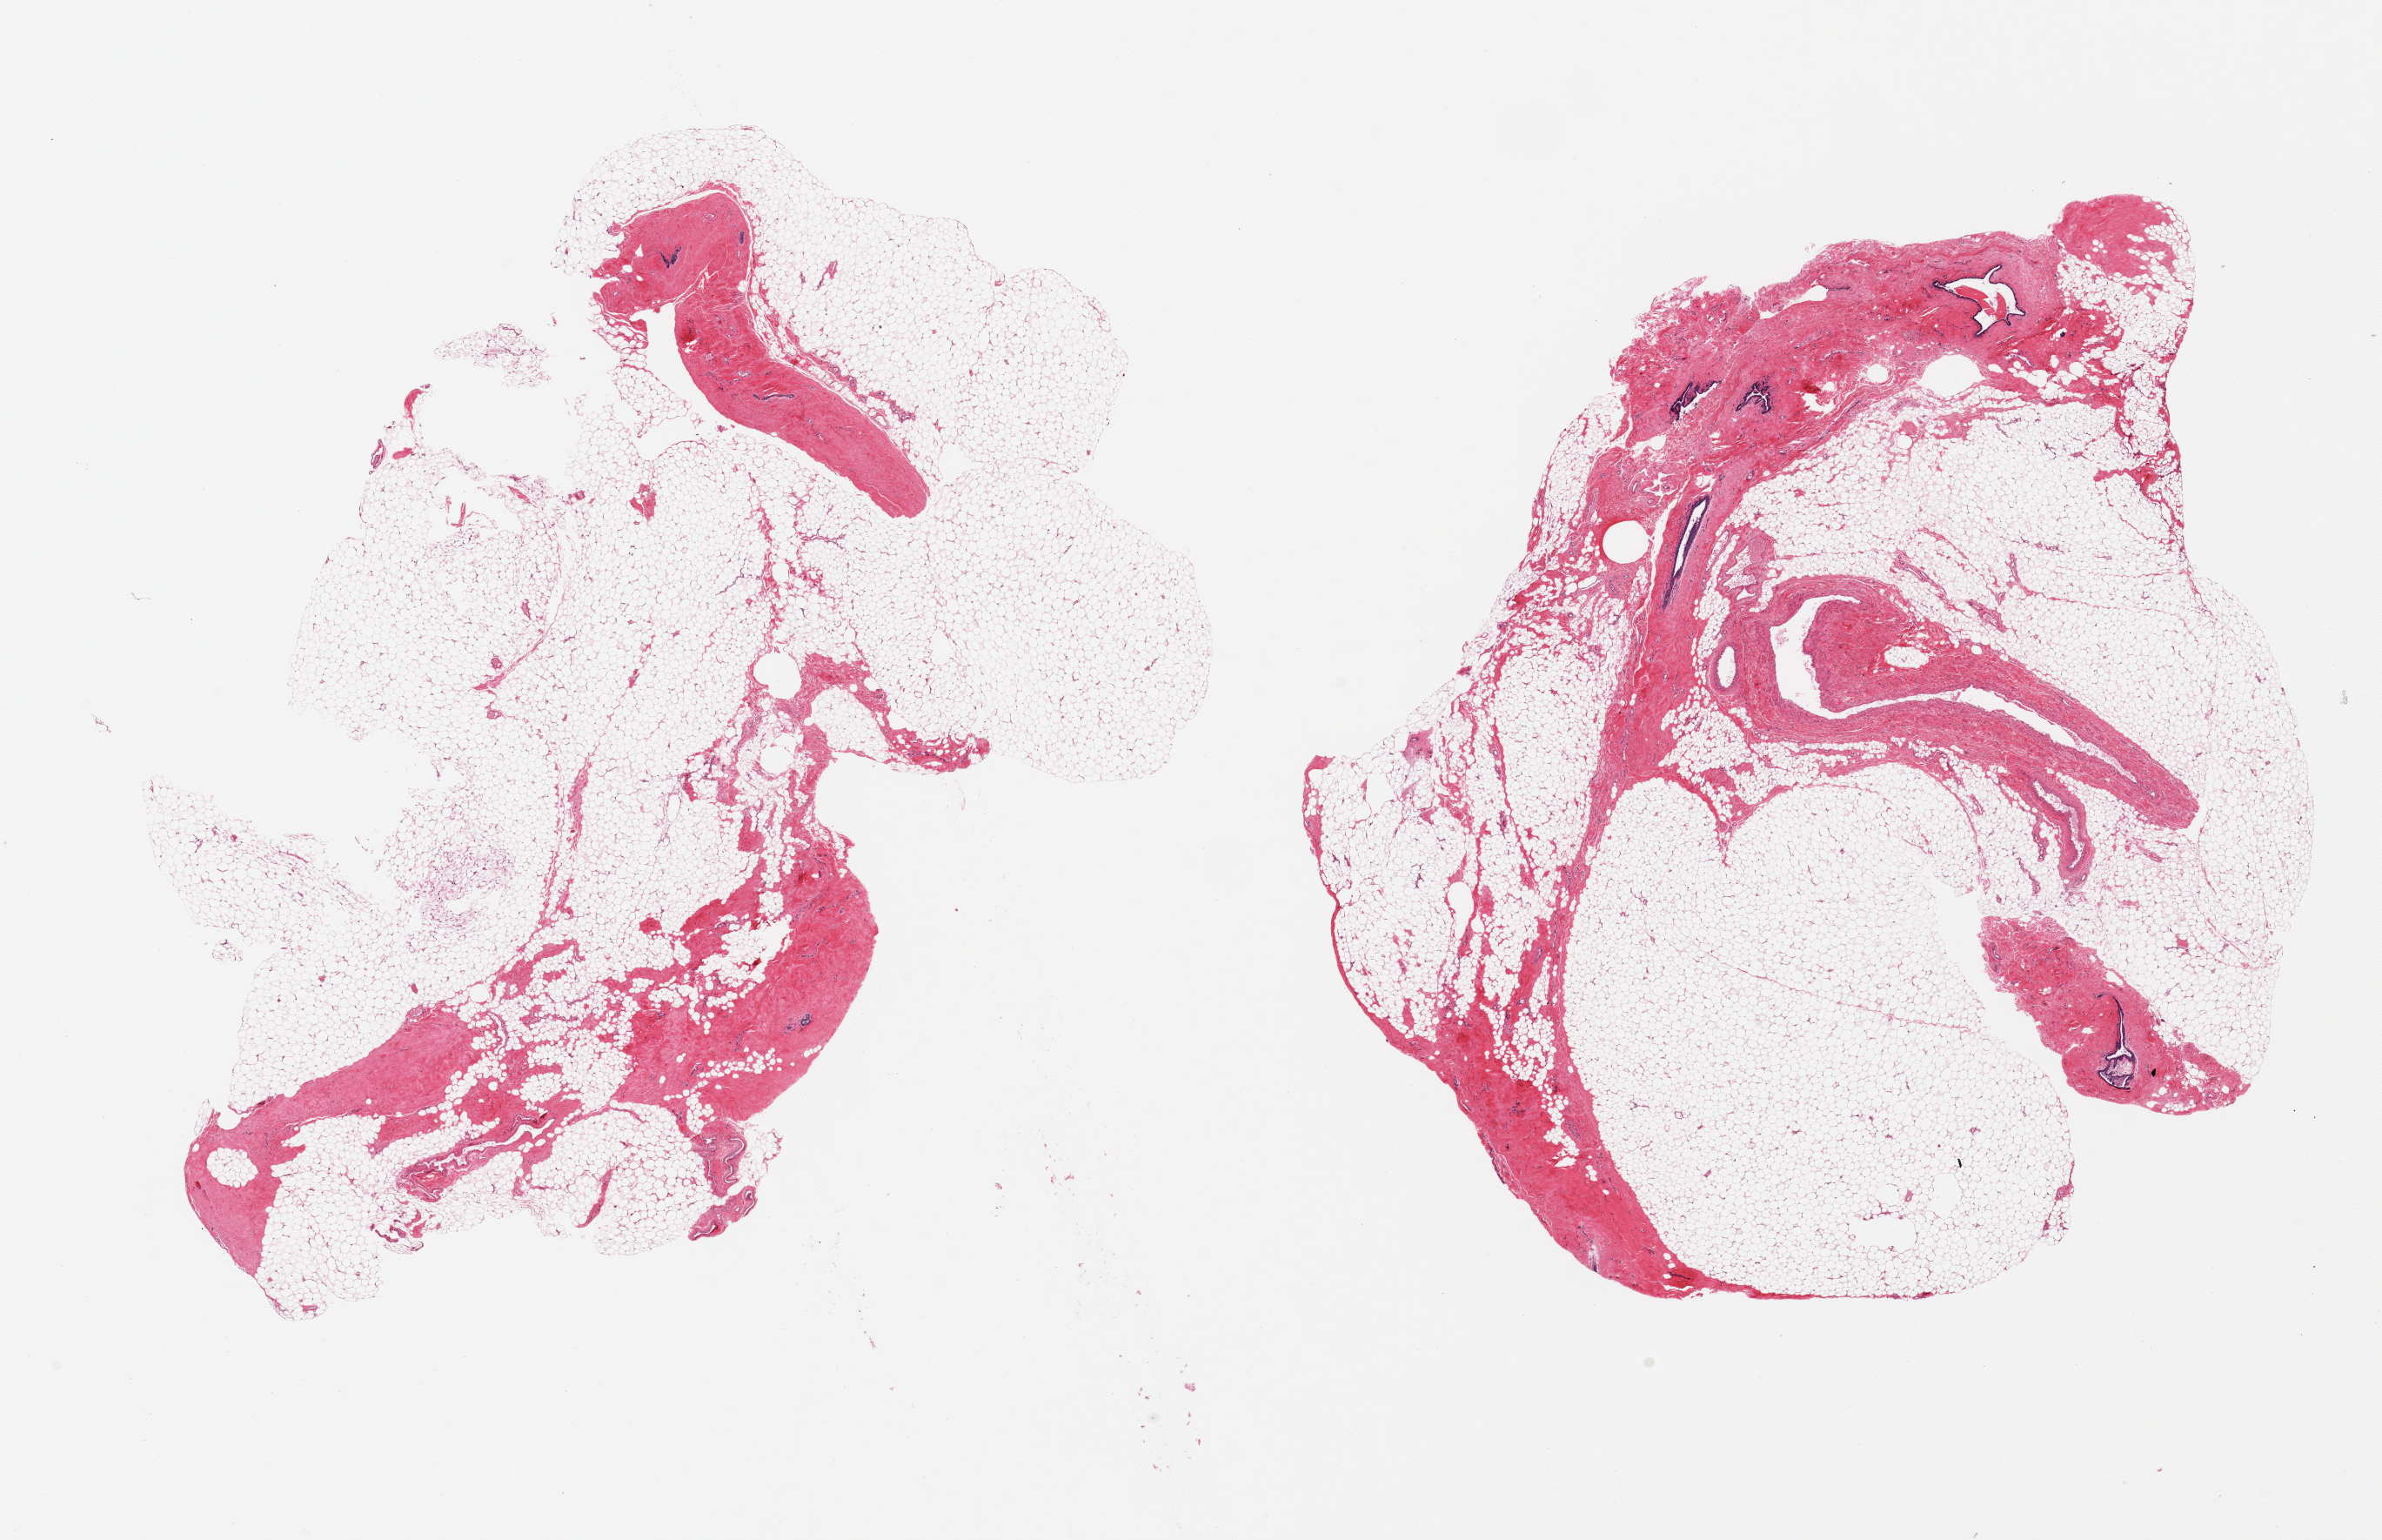
Hematoxylin and eosin (H&E) whole-slide image, brightfield, a low-resolution overview of the entire scanned area, about 21.7 x 14.0 mm; PAXgene-fixed, paraffin-embedded tissue; section of breast (target tissue); donor tissue sample.
Reviewer comment on this tissue sample: 2 pieces, ~11x6mm, largely fibroadipose, rare ductal elements.